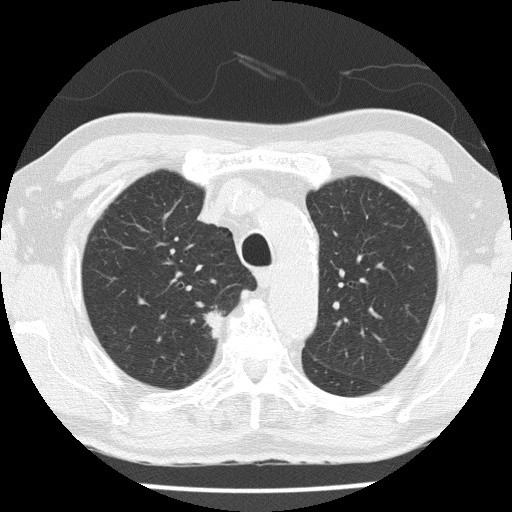
Low-dose screening chest CT, one axial slice; position 112 of 153 along the scan axis; reconstruction kernel FC51; lung window (W 1500 / L -600 HU); 512 × 512 image matrix, field of view 323 × 323 mm.
Structures marked on this image (manually delineated by an expert):
- lesion 1 (tumor, upper lobe of right lung): bounding box <205,311,224,338> (left, top, right, bottom; pixels)